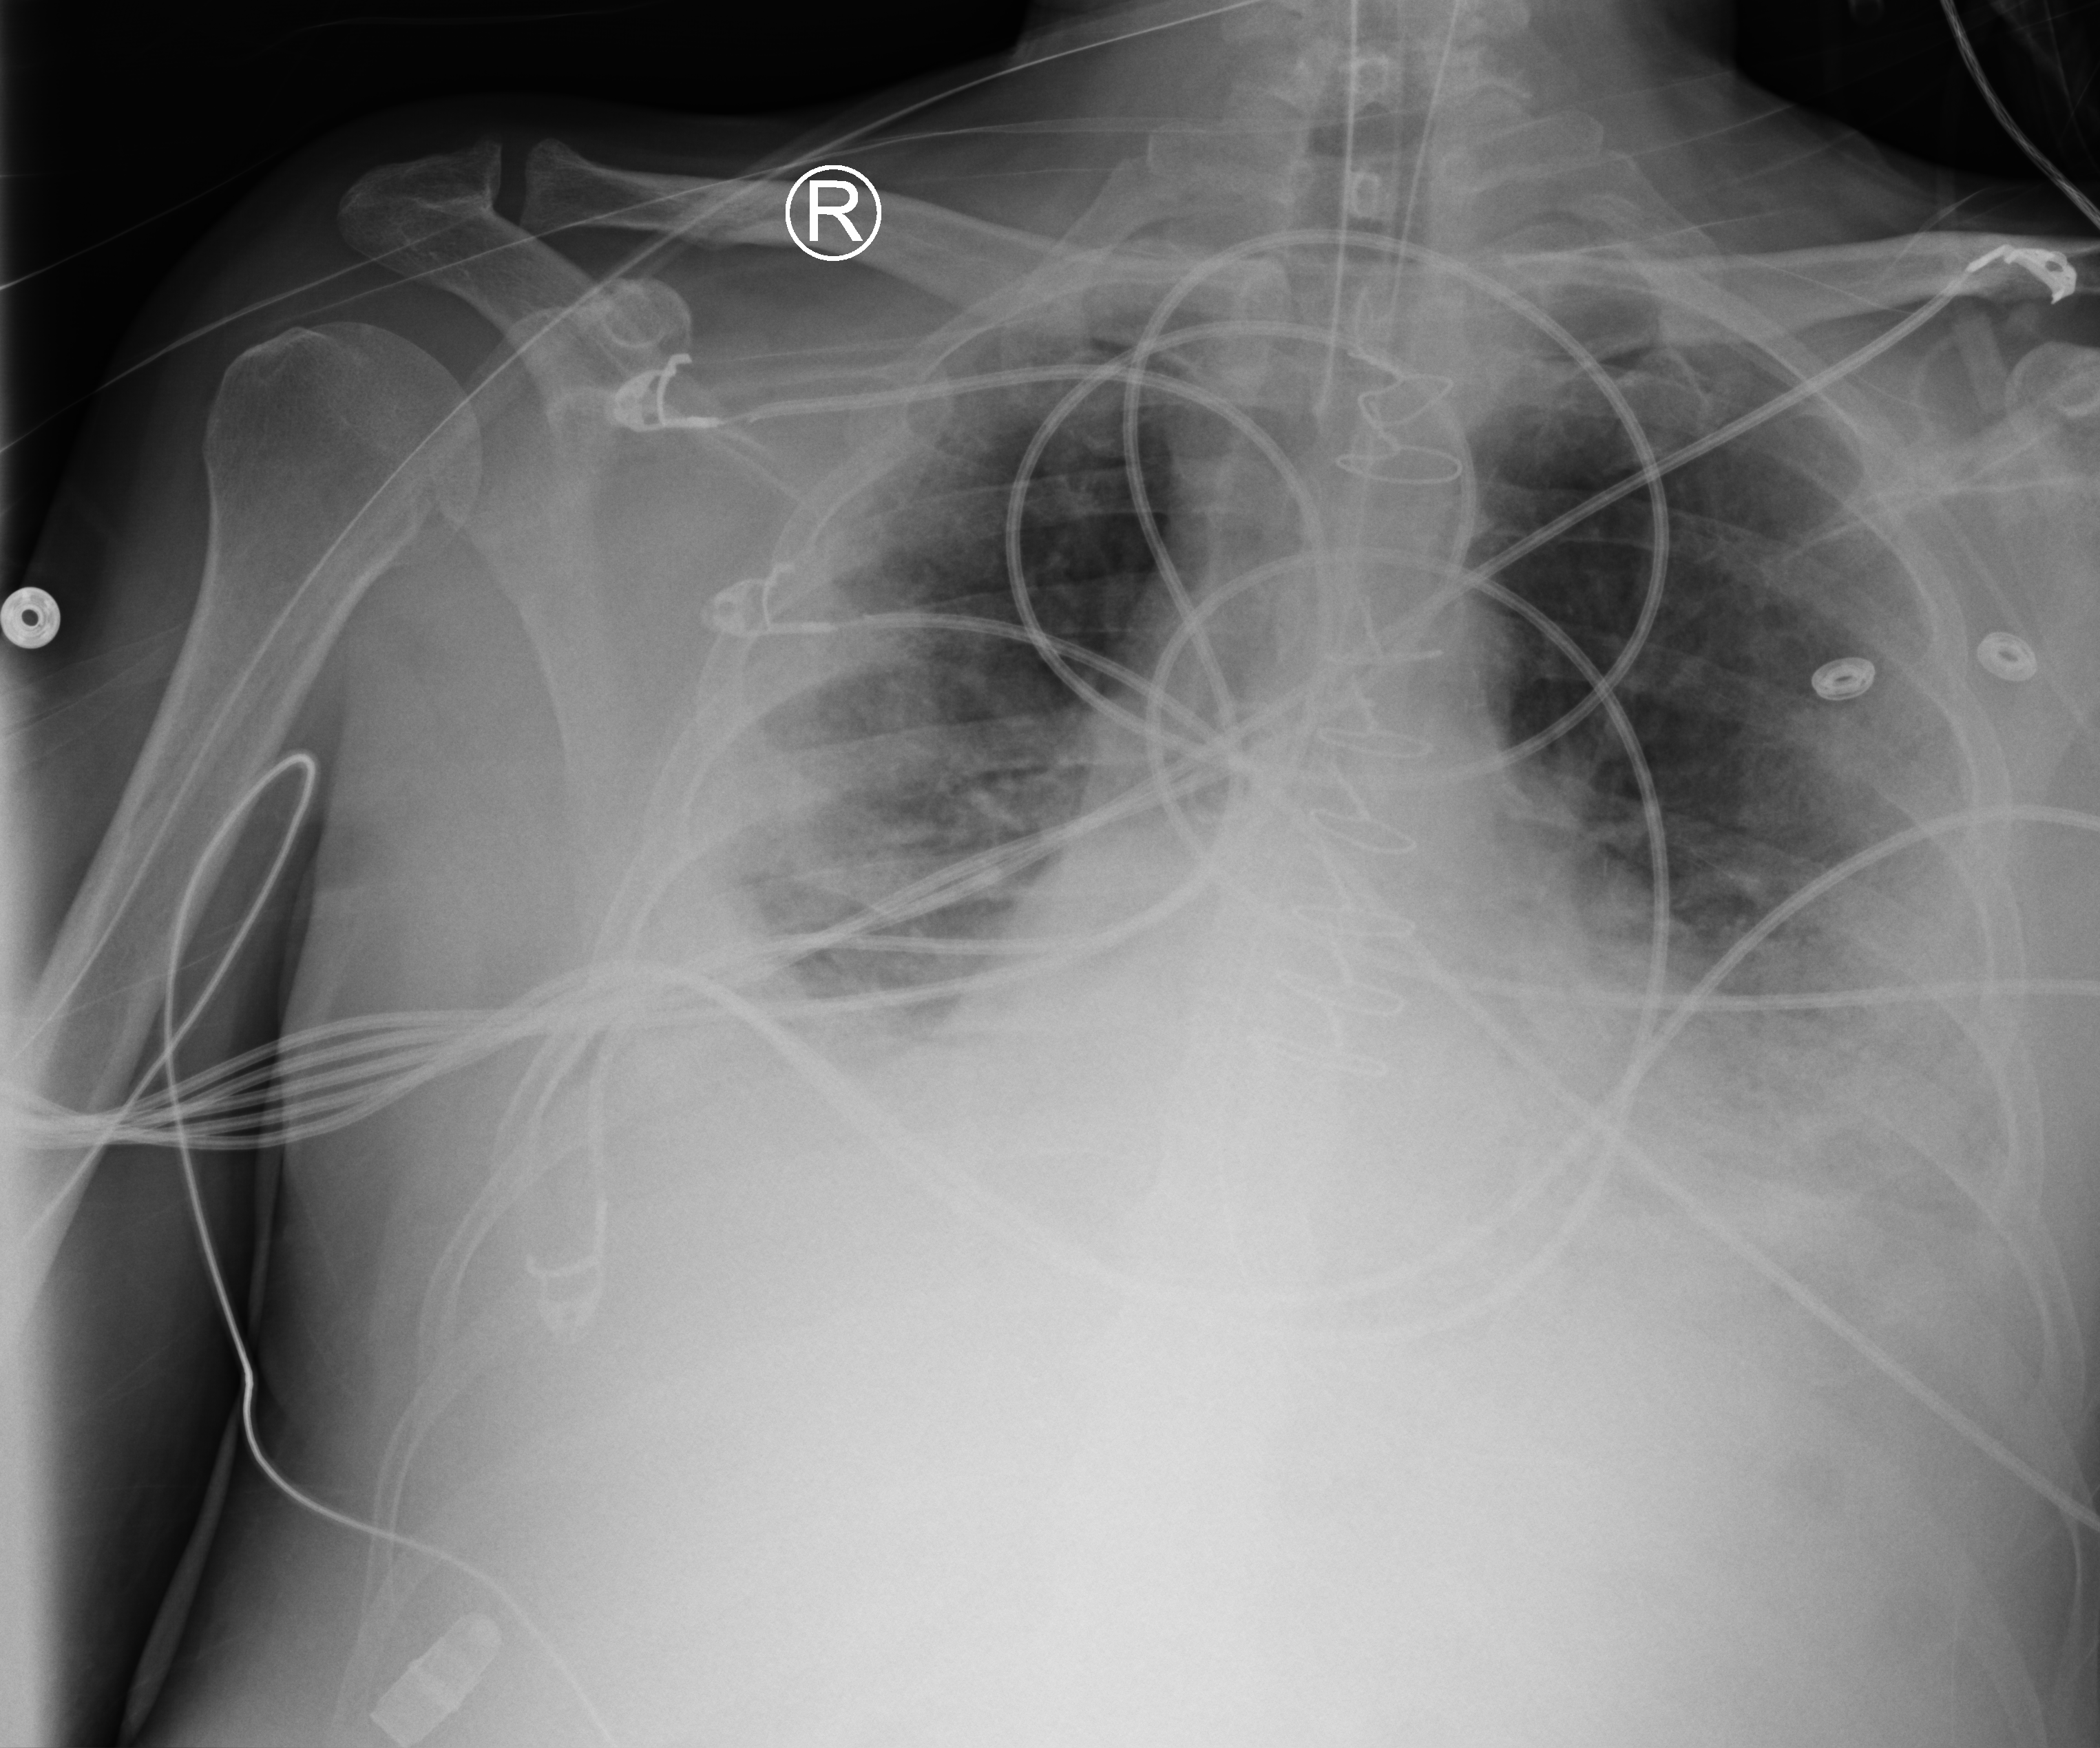
Chest X-ray (portable), anteroposterior (AP) projection. Patient hospitalised with COVID-19; male, aged 18–59 years.
Hospital-stay facts (about this admission, not read from this image; timing relative to this image not recorded):
- admitted to intensive care during this hospital stay: yes